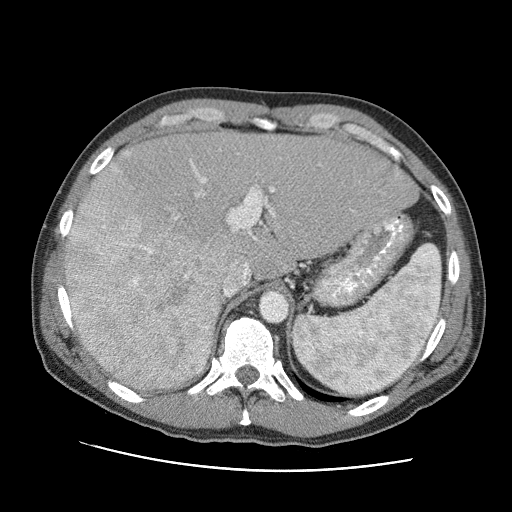
Contrast-enhanced abdominal CT (liver protocol), one axial slice. Position 65 of 95 along the scan axis. One of 2 acquisitions stored at this slice position. Soft-tissue window (W 400 / L 40 HU). 2.5 mm slice thickness. 512 × 512 image matrix, field of view 360 × 360 mm. From the clinical record (not read from this slice): diagnosis: hepatocellular carcinoma (patient treated with transarterial chemoembolisation; whether this scan precedes or follows treatment is not stated here); TNM stage (as recorded): Stage-IVA; Child-Pugh class: A; tumour nodularity: multinodular.
Structures marked on this image (semi-automatic segmentation, software-assisted and operator-edited):
- liver parenchyma outside the tumour (the mass and vessels are separate outlines, so this box may not span the whole liver): box from (x=66, y=130) to (x=418, y=388) px
- mass: (x=64, y=160)–(x=224, y=394)
- liver vessels: (x=124, y=151)–(x=275, y=285)